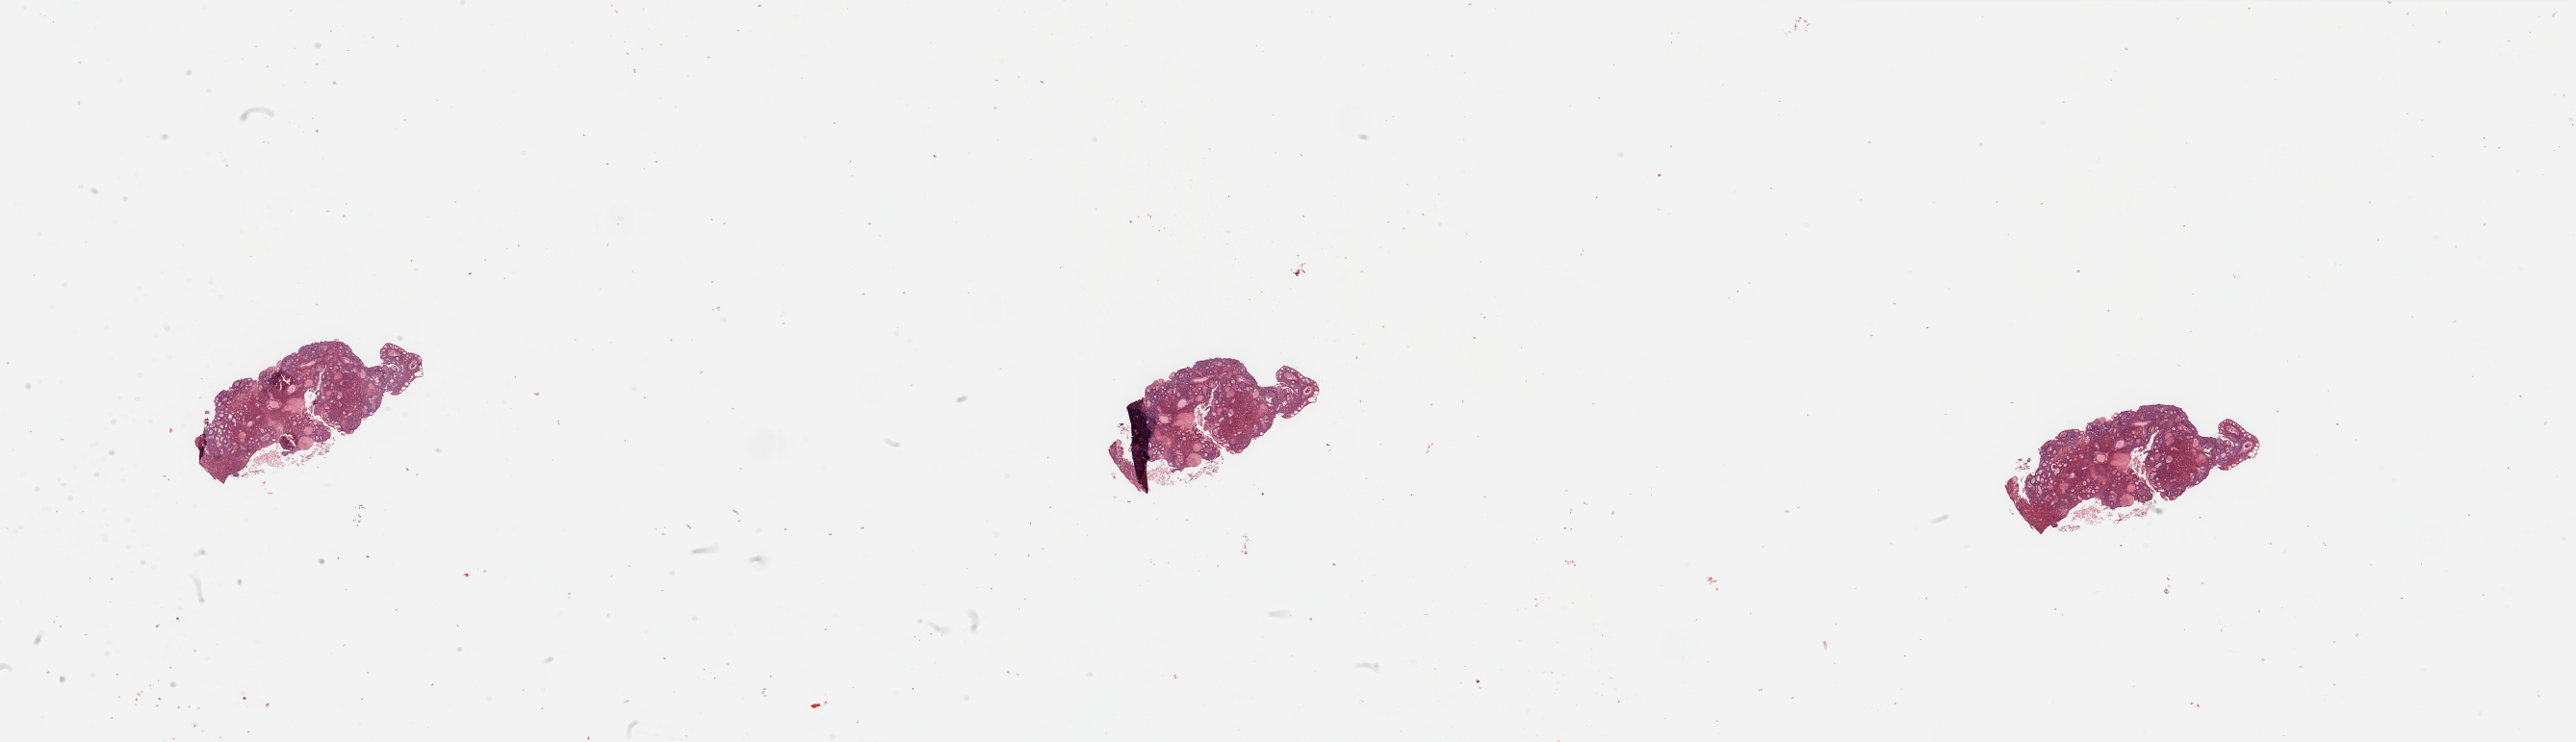
Whole-slide histology image, H&E, whole scanned area (about 42.3 x 12.2 mm) shown as a low-resolution overview; tumour tissue sample, sampled site: uterus. Female, 63 y/o. Composition of this section per pathologist review: tumour nuclei 80%, necrosis 0%.
Diagnosis: Endometrioid adenocarcinoma, NOS.